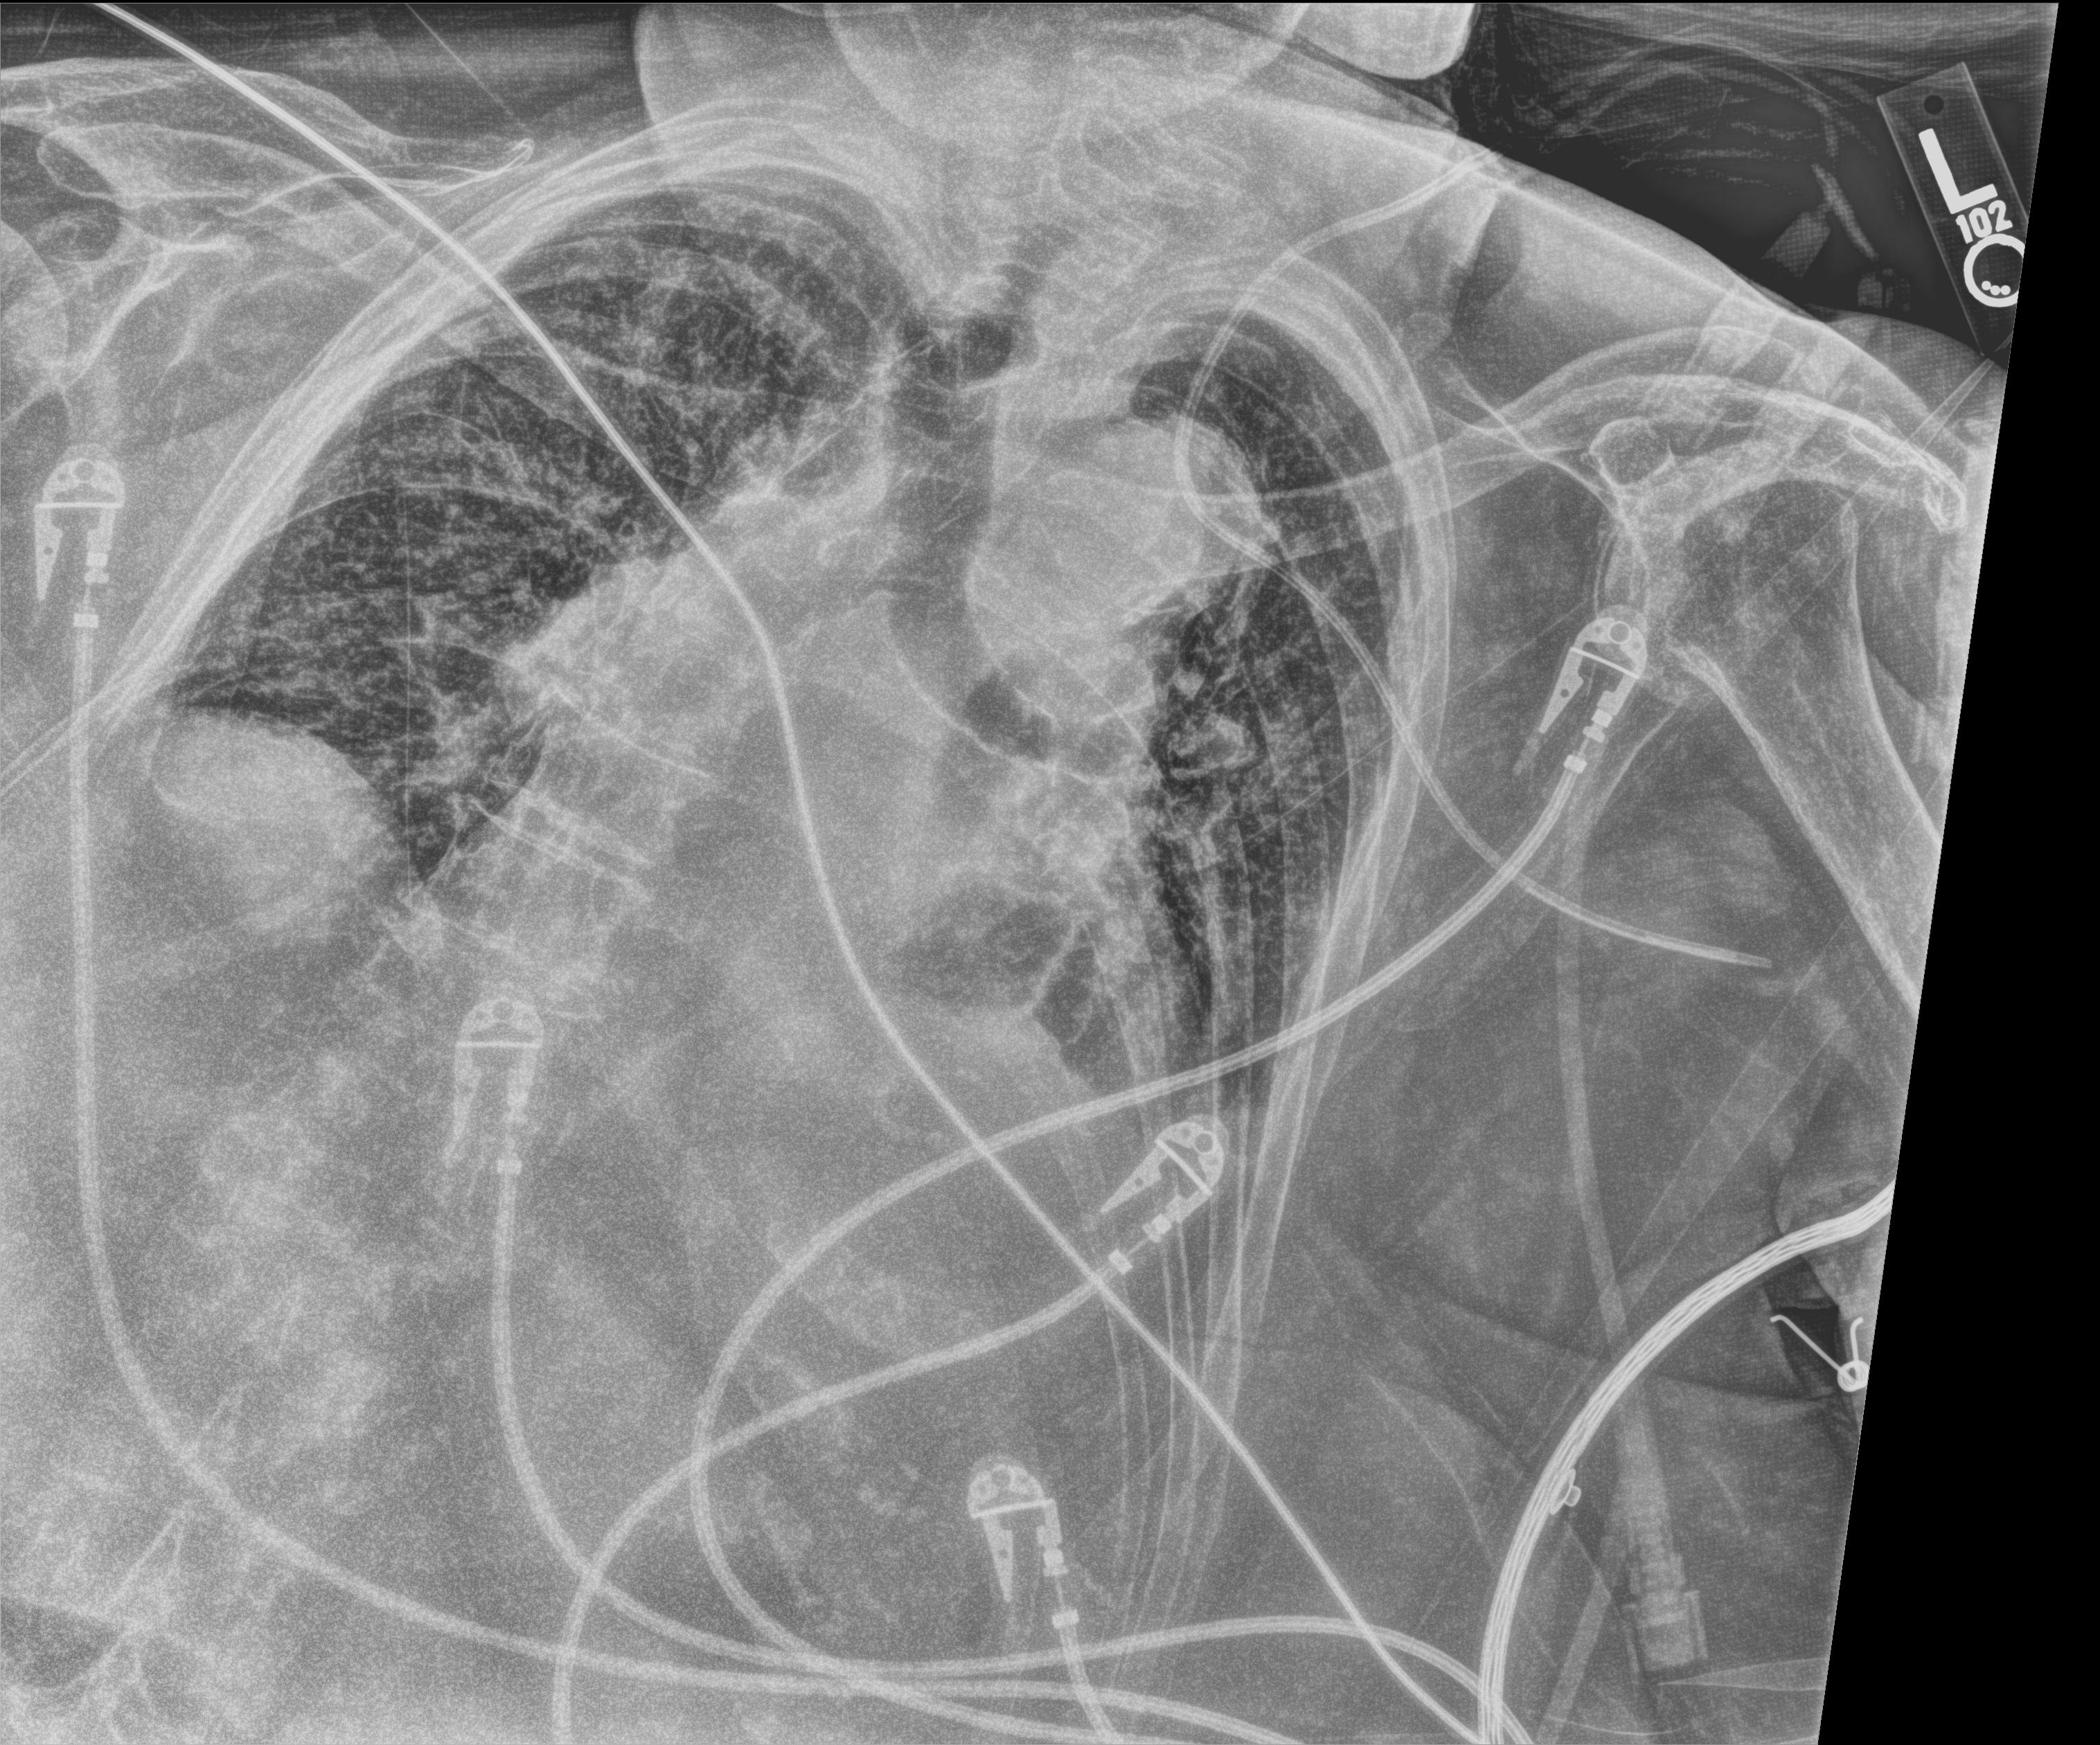
Chest X-ray (portable); anteroposterior (AP) projection. Female patient hospitalised with COVID-19, age 75–90 years.
Admission-level facts for this patient (not findings on this image; timing relative to this image not recorded): mechanically ventilated during this hospital stay: no.